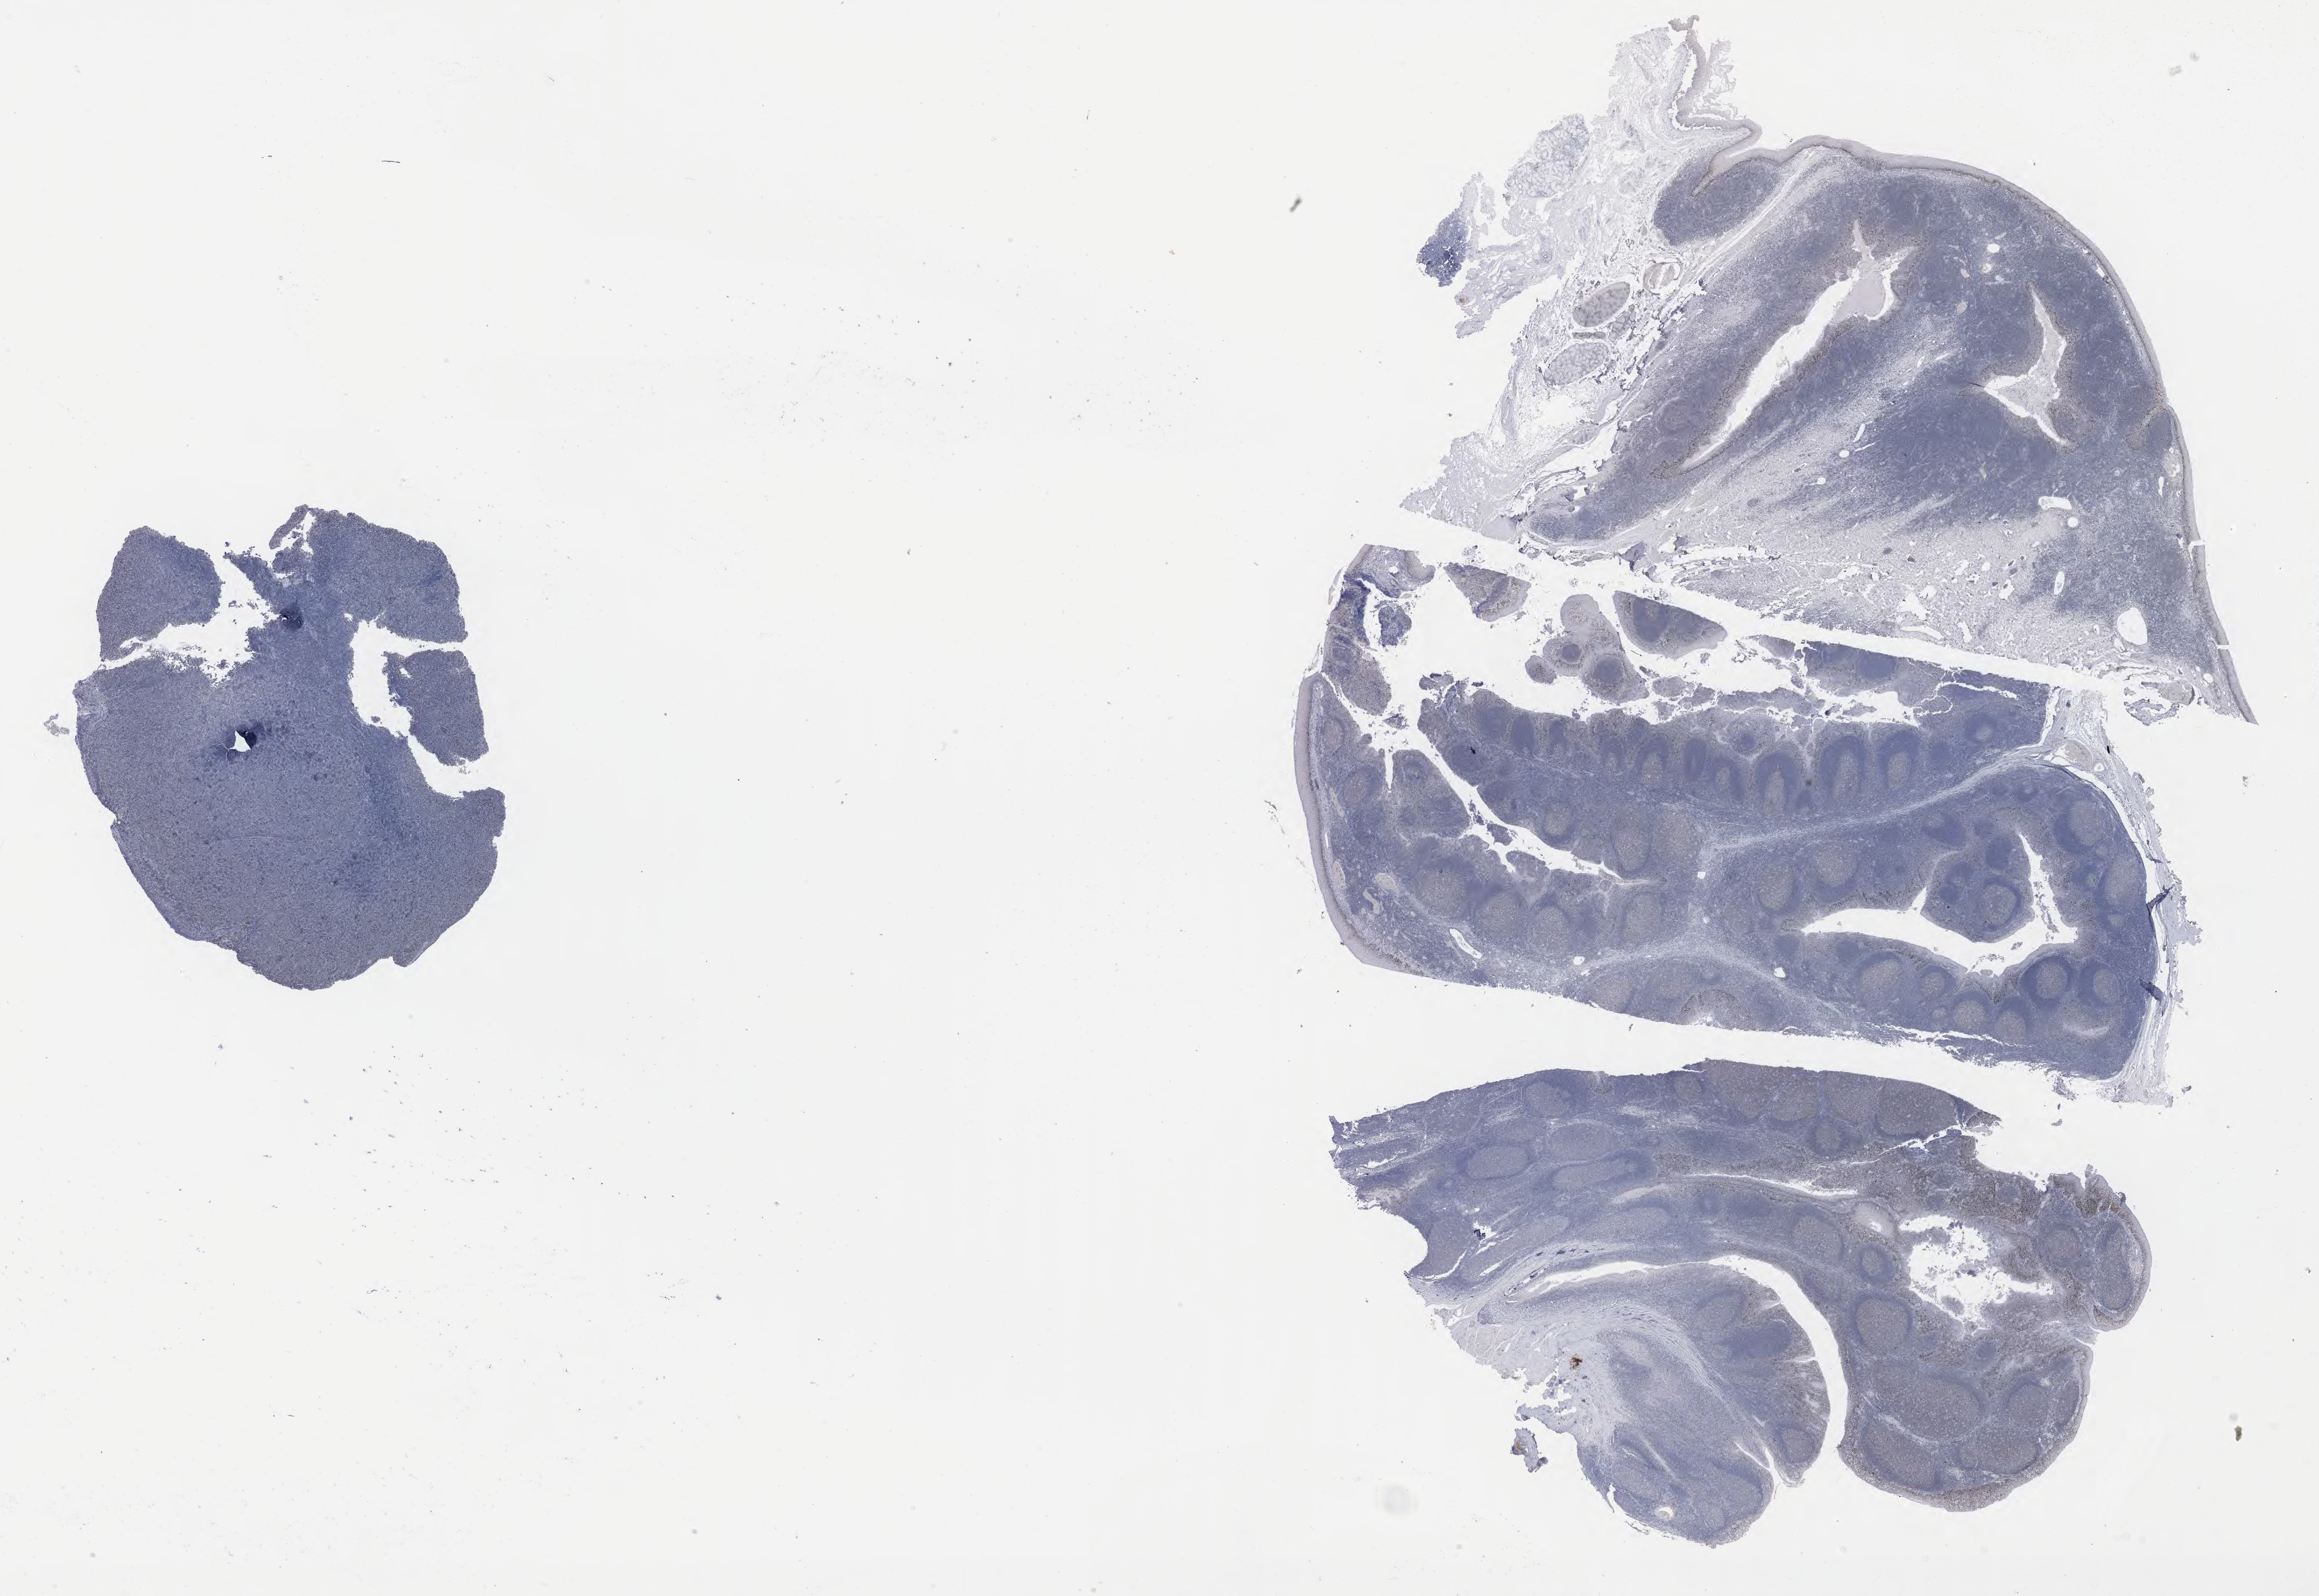
Immunohistochemistry (IHC) whole-slide image stained for p53, low-resolution overview of the scanned area, about 32.2 x 22.2 mm. Tumor tissue. Anatomic site: liver. Patient male; aged 46.
Diagnosis: Diffuse large B-cell lymphoma, NOS.